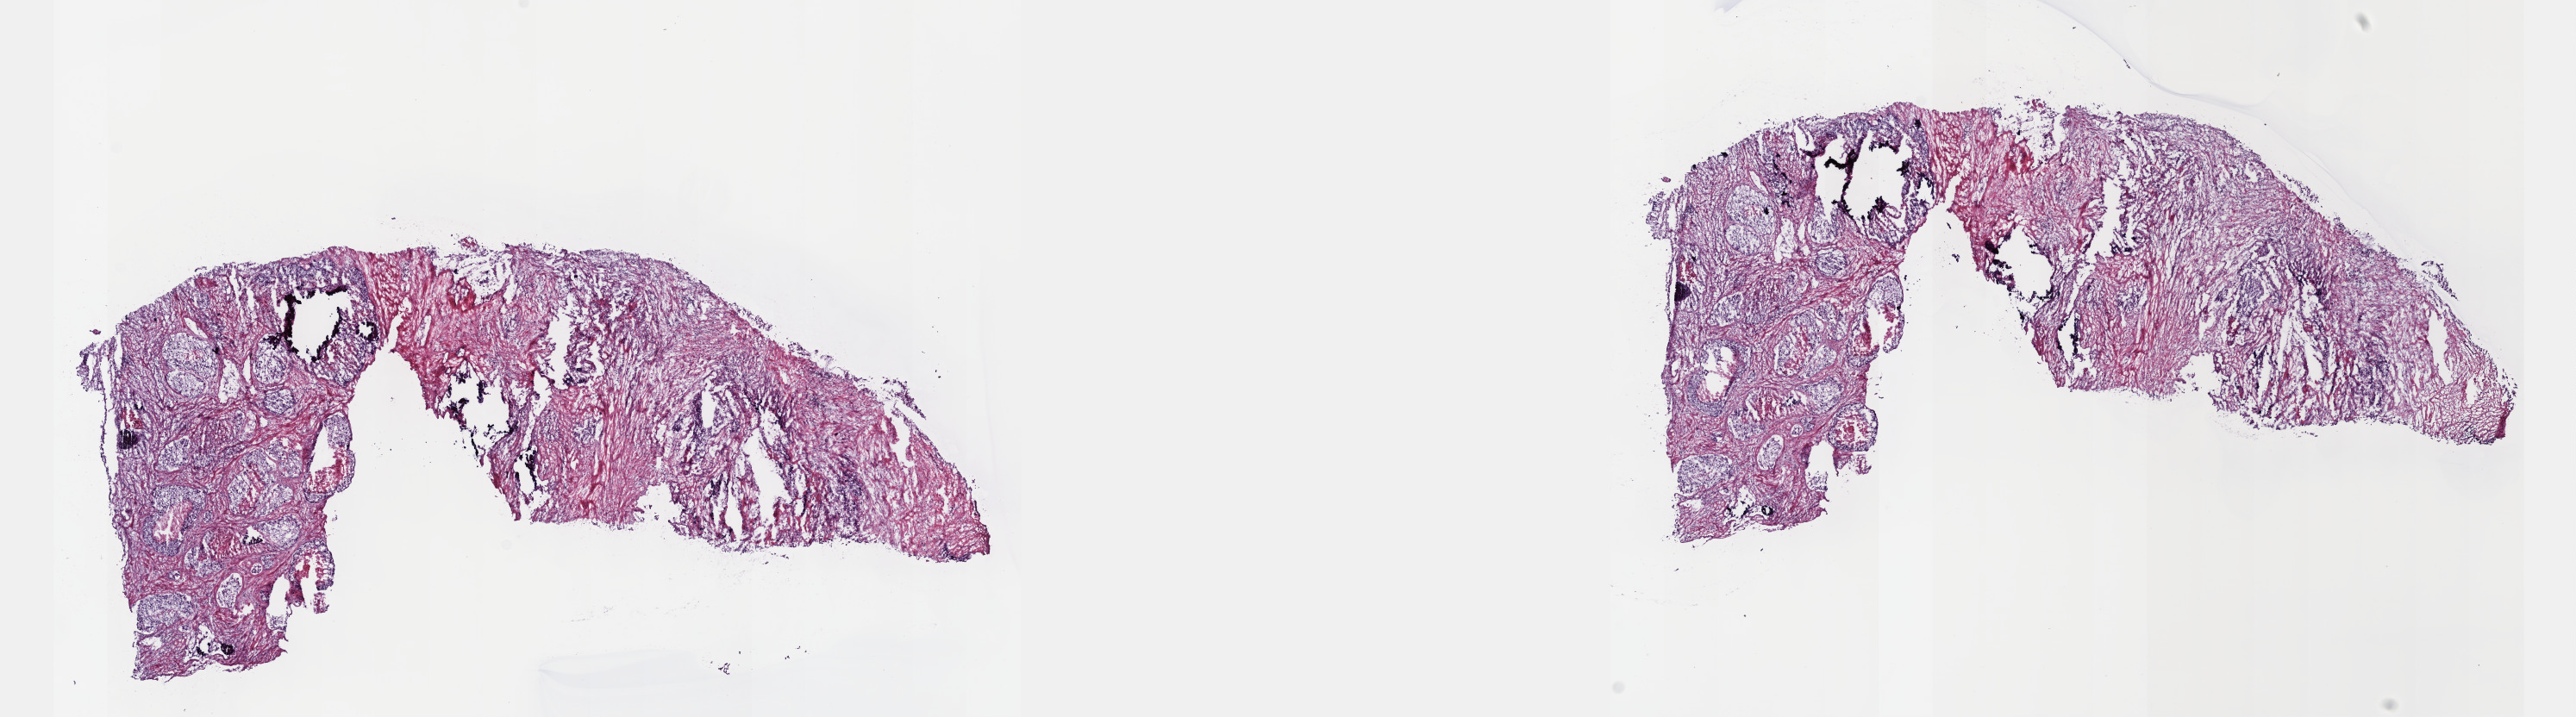
Whole-slide histology image, H&E-stained, low-resolution overview of the scanned area, about 24.1 x 6.7 mm (acquisition: 40x scan). Frozen section. Primary tumour sample from the prostate. Patient: male, age at initial diagnosis 64 years. Gleason score: 8 (4+4). Pathologist review of this section (percent, as recorded): tumour cells 60%, tumour nuclei 60%, normal cells 10%, stromal cells 30%, necrosis 0%. Infiltration values recorded for this section: lymphocyte infiltration 40%, monocyte infiltration 20%, neutrophil infiltration 20%.
Pathologic diagnosis: Adenocarcinoma, NOS (prostate gland). Lymph nodes positive (case pathology): 0 of 4 examined. Laterality: bilateral.